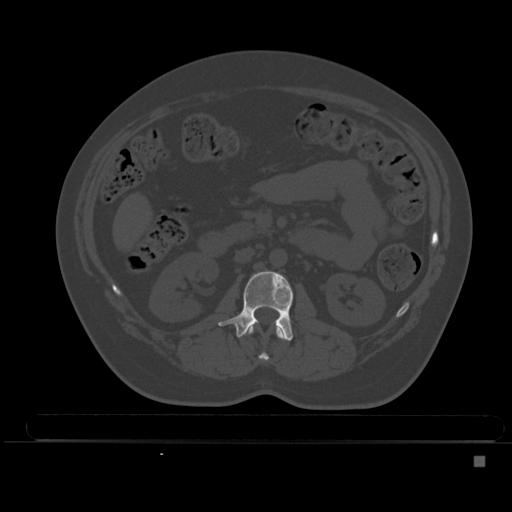
CT including the spine, one axial slice. Position 179 of 495 along the scan axis. Bone window (W 1800 / L 400 HU). 1.5 mm slice thickness. 512 × 512 image matrix, field of view 404 × 404 mm. Patient: female, 33 years. From the clinical record (not read from this slice): primary cancer: breast; vertebrae with lytic lesions (as recorded): T1.
Outlined on this slice (semi-automatically segmented with operator editing):
- L1 vertebra: bounding box [x1, y1, x2, y2] px = [246, 326, 285, 361]
- L2 vertebra: [218, 271, 294, 341]